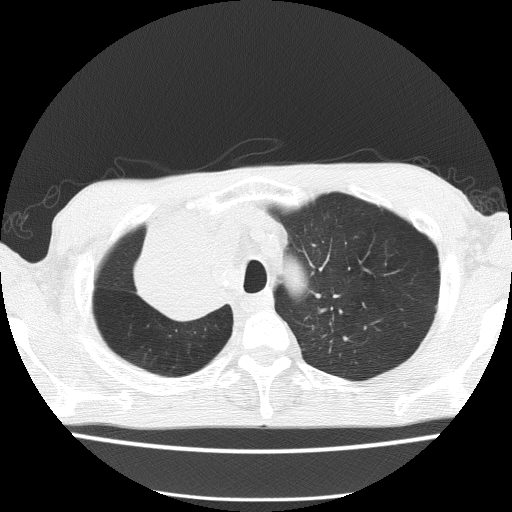
Low-dose screening chest CT, one axial slice. Slice 120 of 150 in the series (ordered by position). Reconstruction kernel FC51. Lung window (W 1500 / L -600 HU). 512 × 512 image matrix, field of view 336 × 336 mm.
Outlined on this slice (outlined manually by an expert reader):
- lesion 1 (tumor, hilum of right lung): bounding box <135,214,217,319> (left, top, right, bottom; pixels)